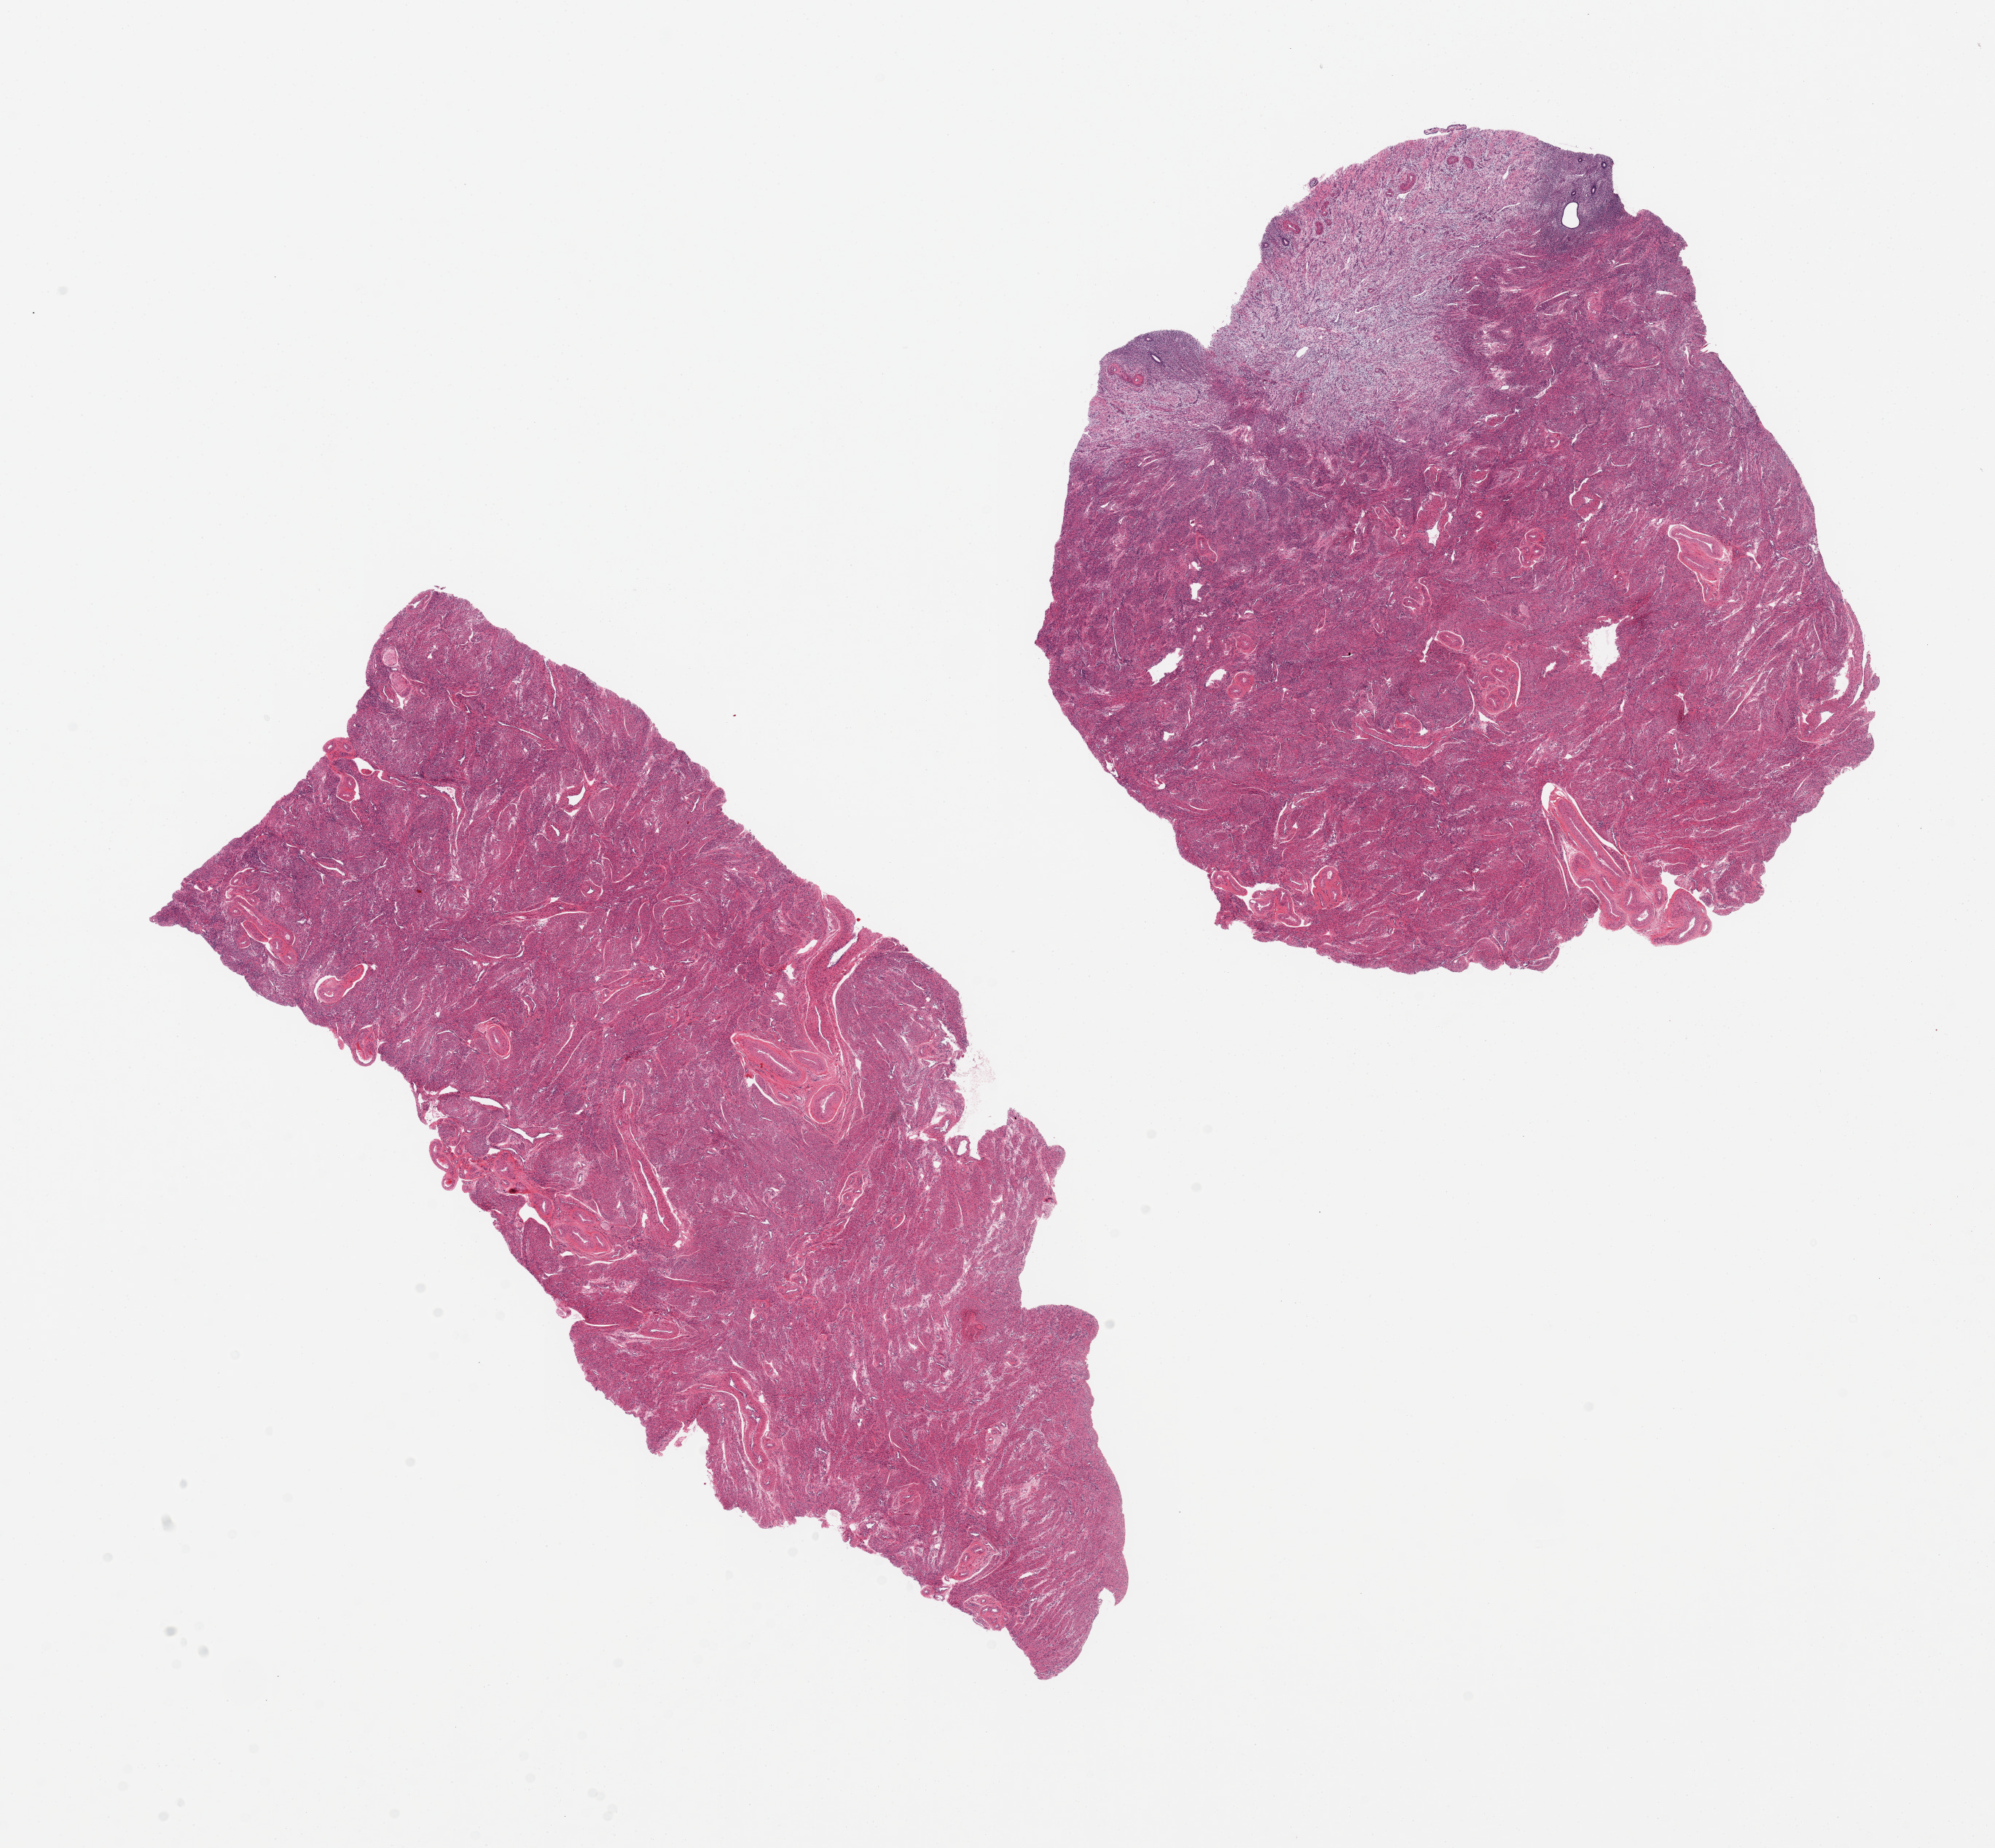
Digitized hematoxylin and eosin (H&E)-stained section, brightfield — a low-resolution overview of the entire scanned area, about 21.7 x 20.1 mm; PAXgene-fixed paraffin-embedded (PFPE) section; sampled site (target tissue): uterus; donor tissue sample. Donor sex: female.
Reviewer comment on this tissue sample: 2 pieces, predominantly myometrium with small portion of endometrium on one piece.